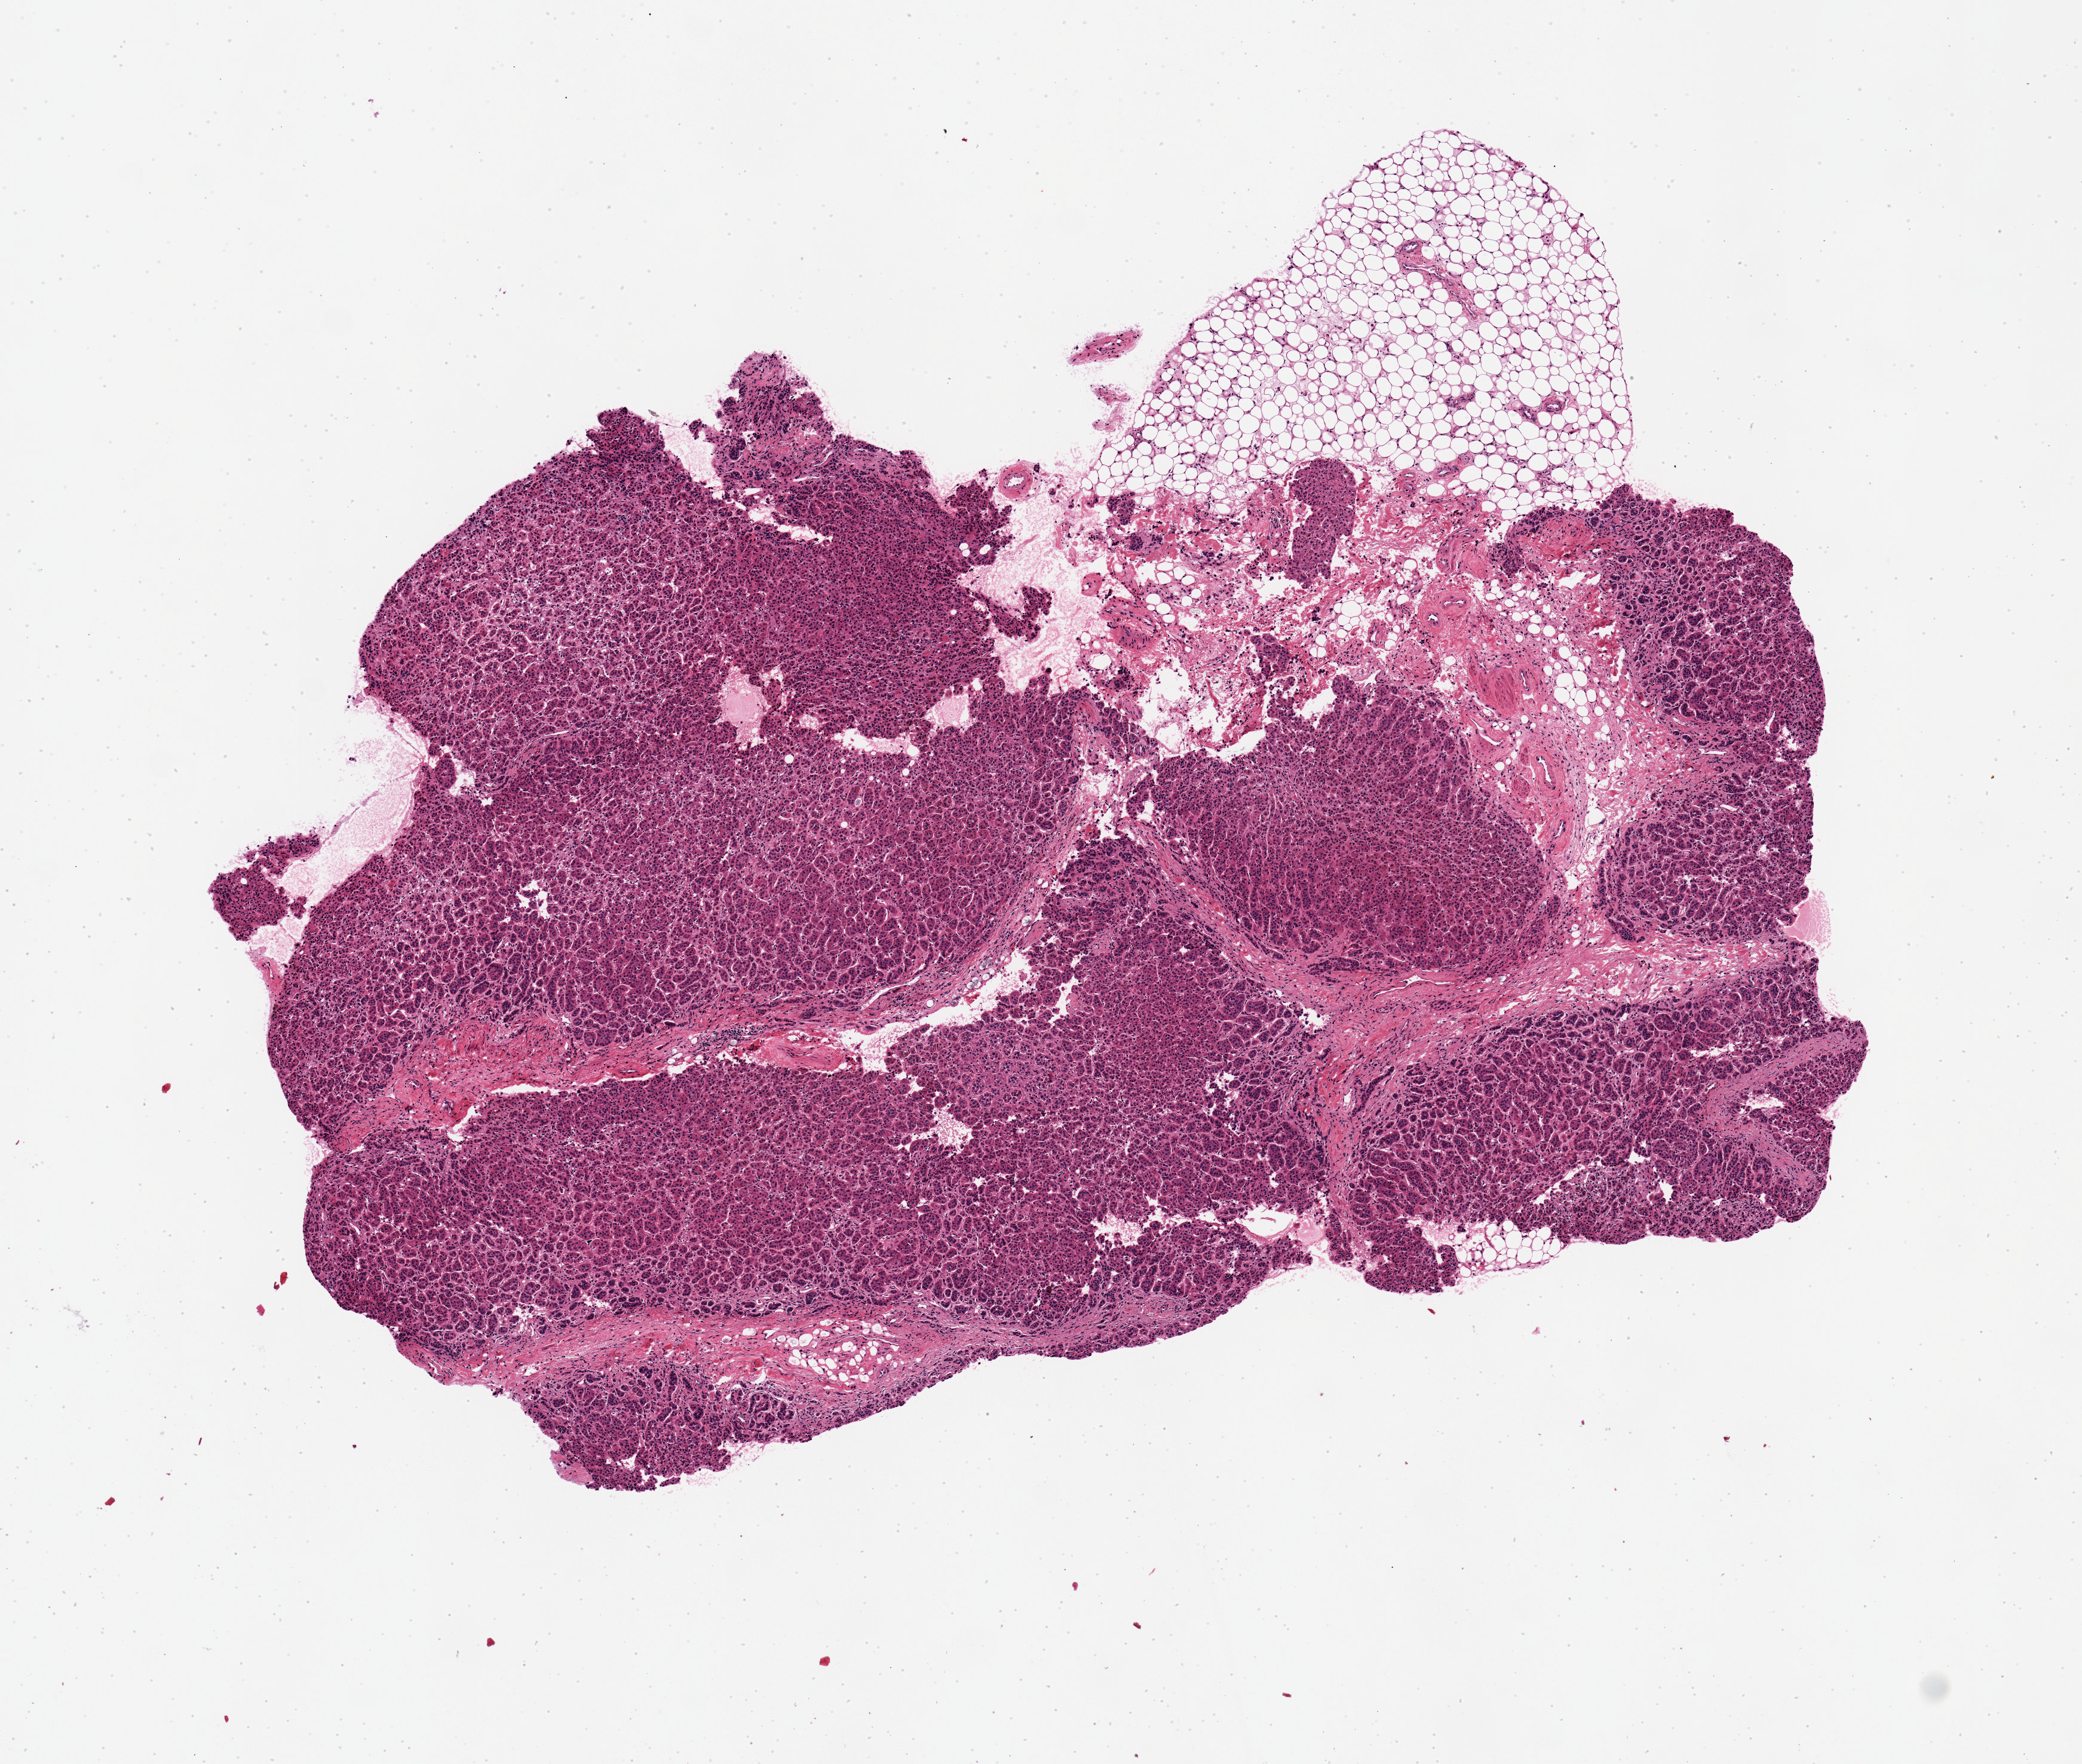
H&E whole-slide image — a low-resolution overview of the entire scanned area, about 6.9 x 5.8 mm; PAXgene-fixed paraffin-embedded (PFPE) section; sampled site (target tissue): adrenal gland; donor tissue sample.
Reviewer comment on this tissue sample: A 1.5x1.0mm nodule fat appends a 3x5mm aliquot.